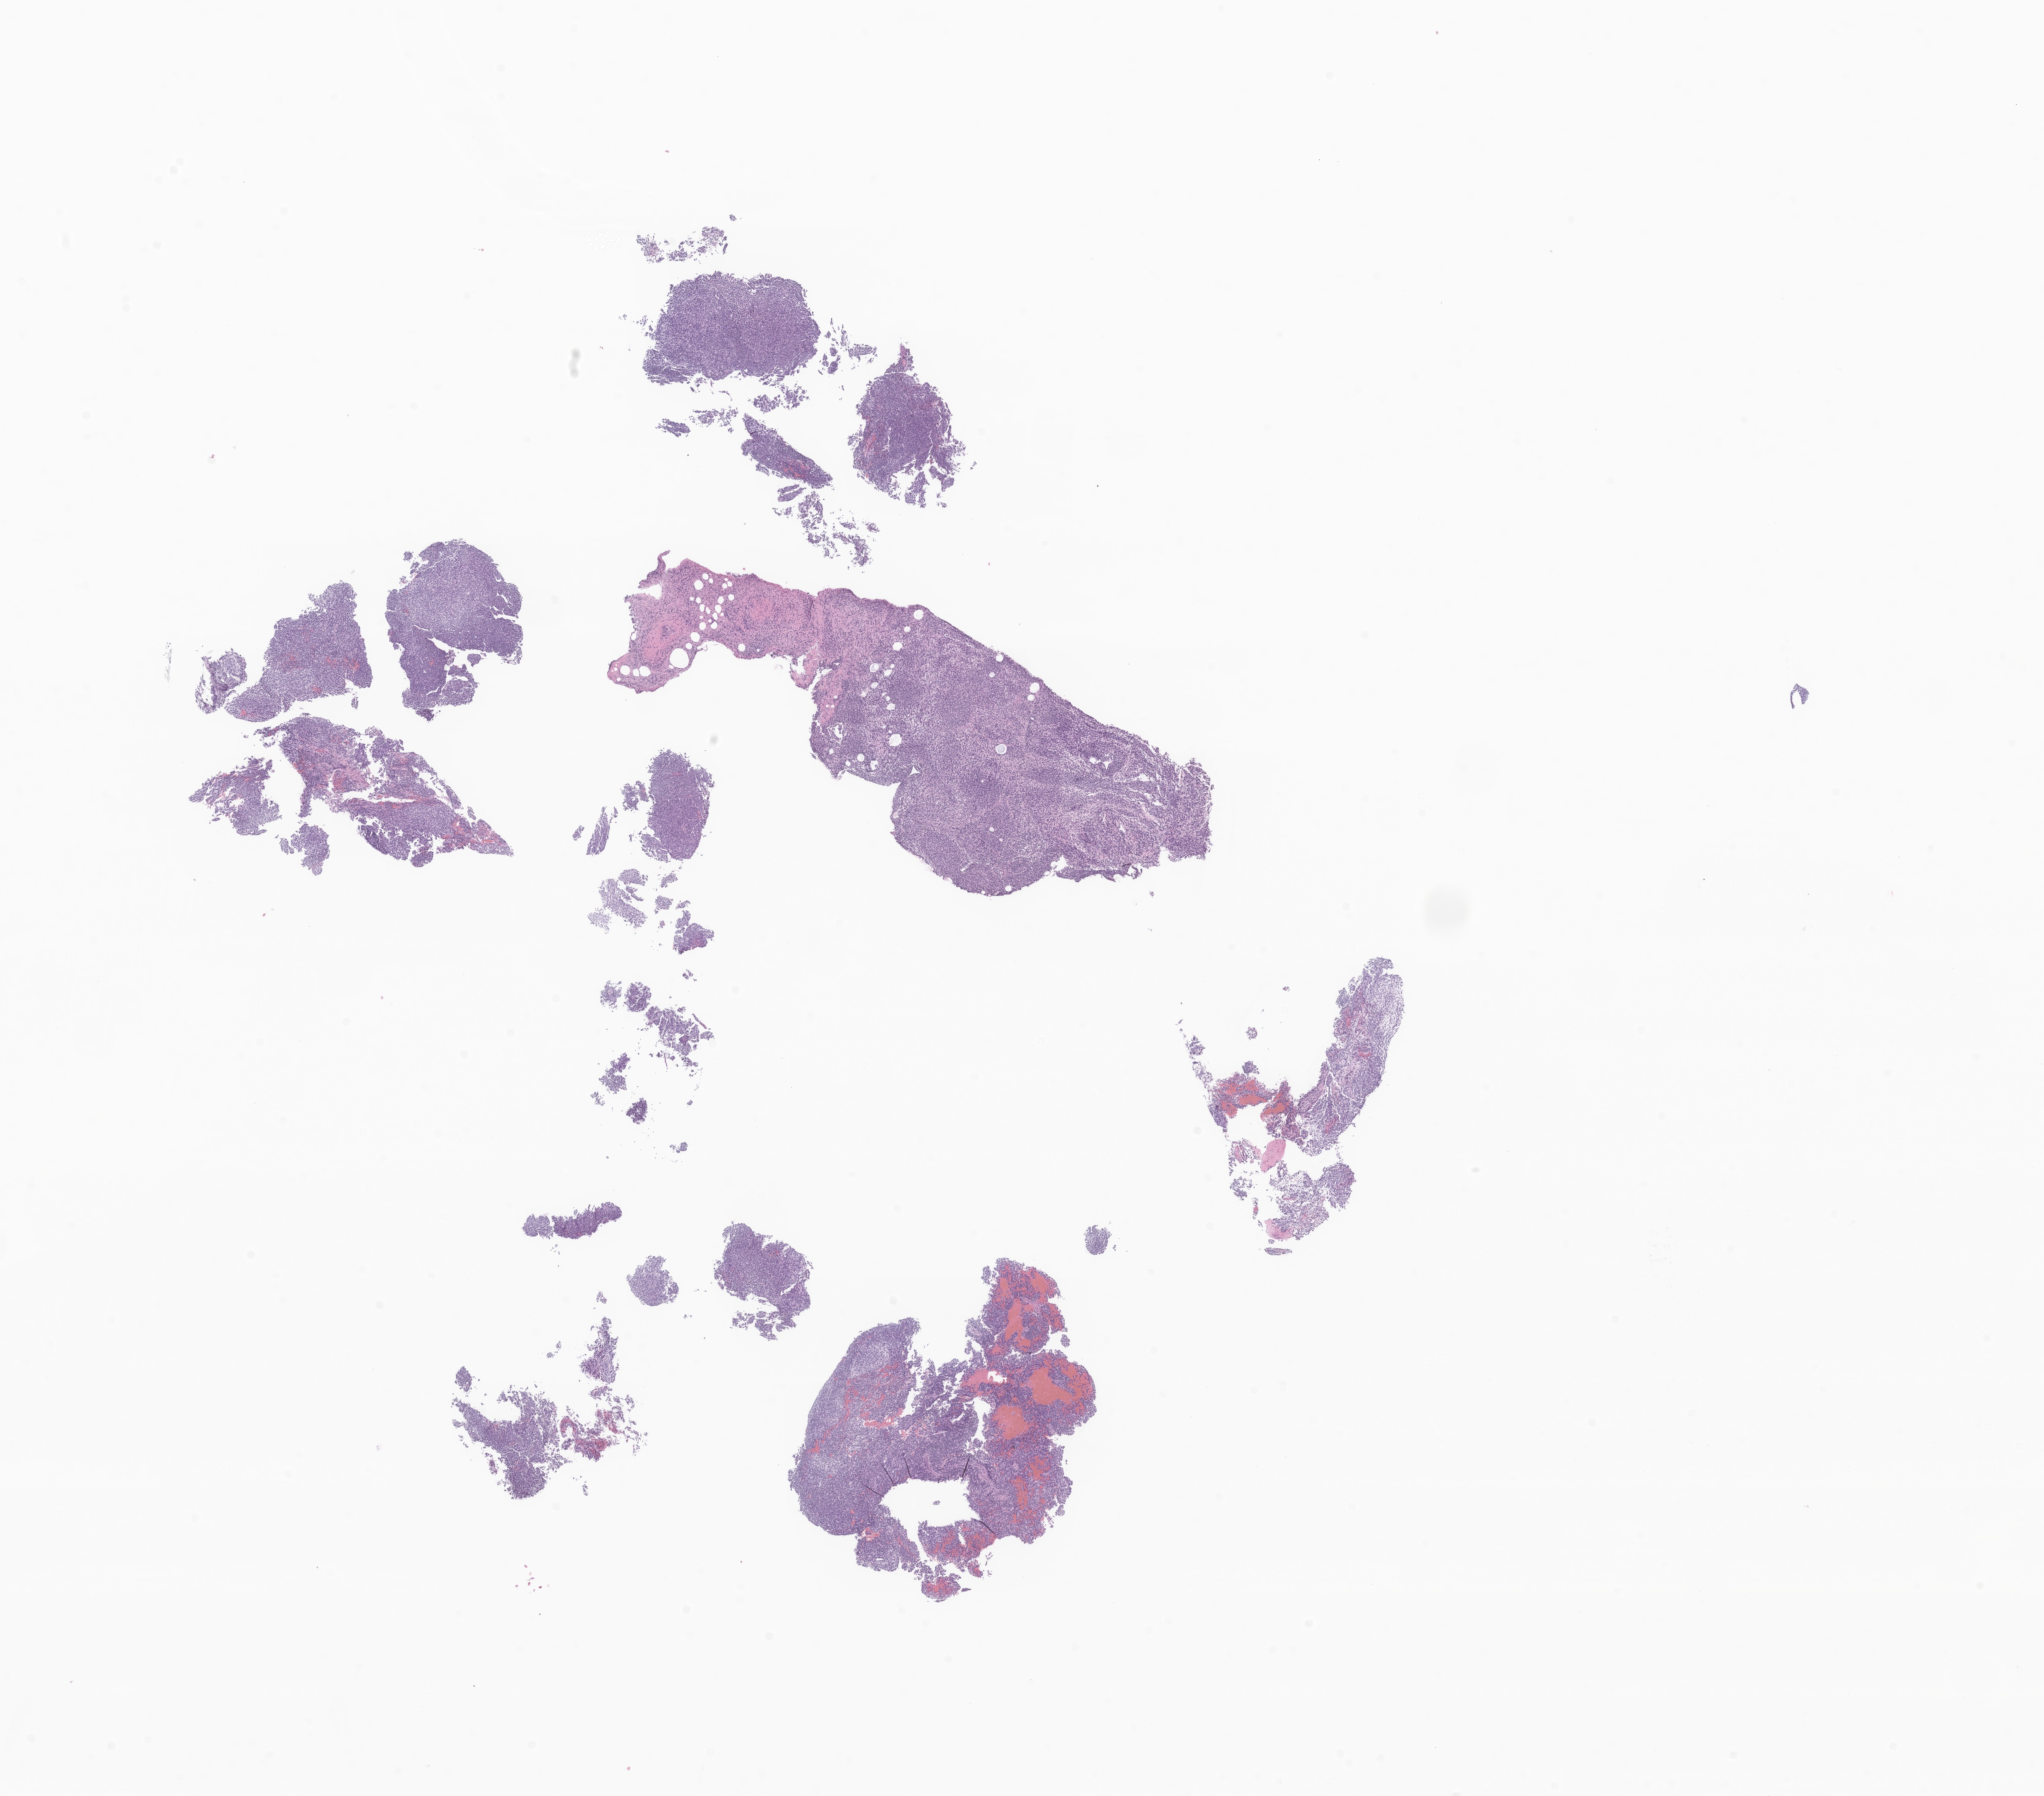
Whole-slide image, haematoxylin and eosin stain of tumor tissue from the cerebellum — whole scanned area (about 20.8 x 18.3 mm) shown as a low-resolution overview. Formalin-fixed, paraffin-embedded (FFPE) tissue. Patient: male, age 101 months (8 years 5 months).
Diagnosis: Medulloblastoma, NOS.